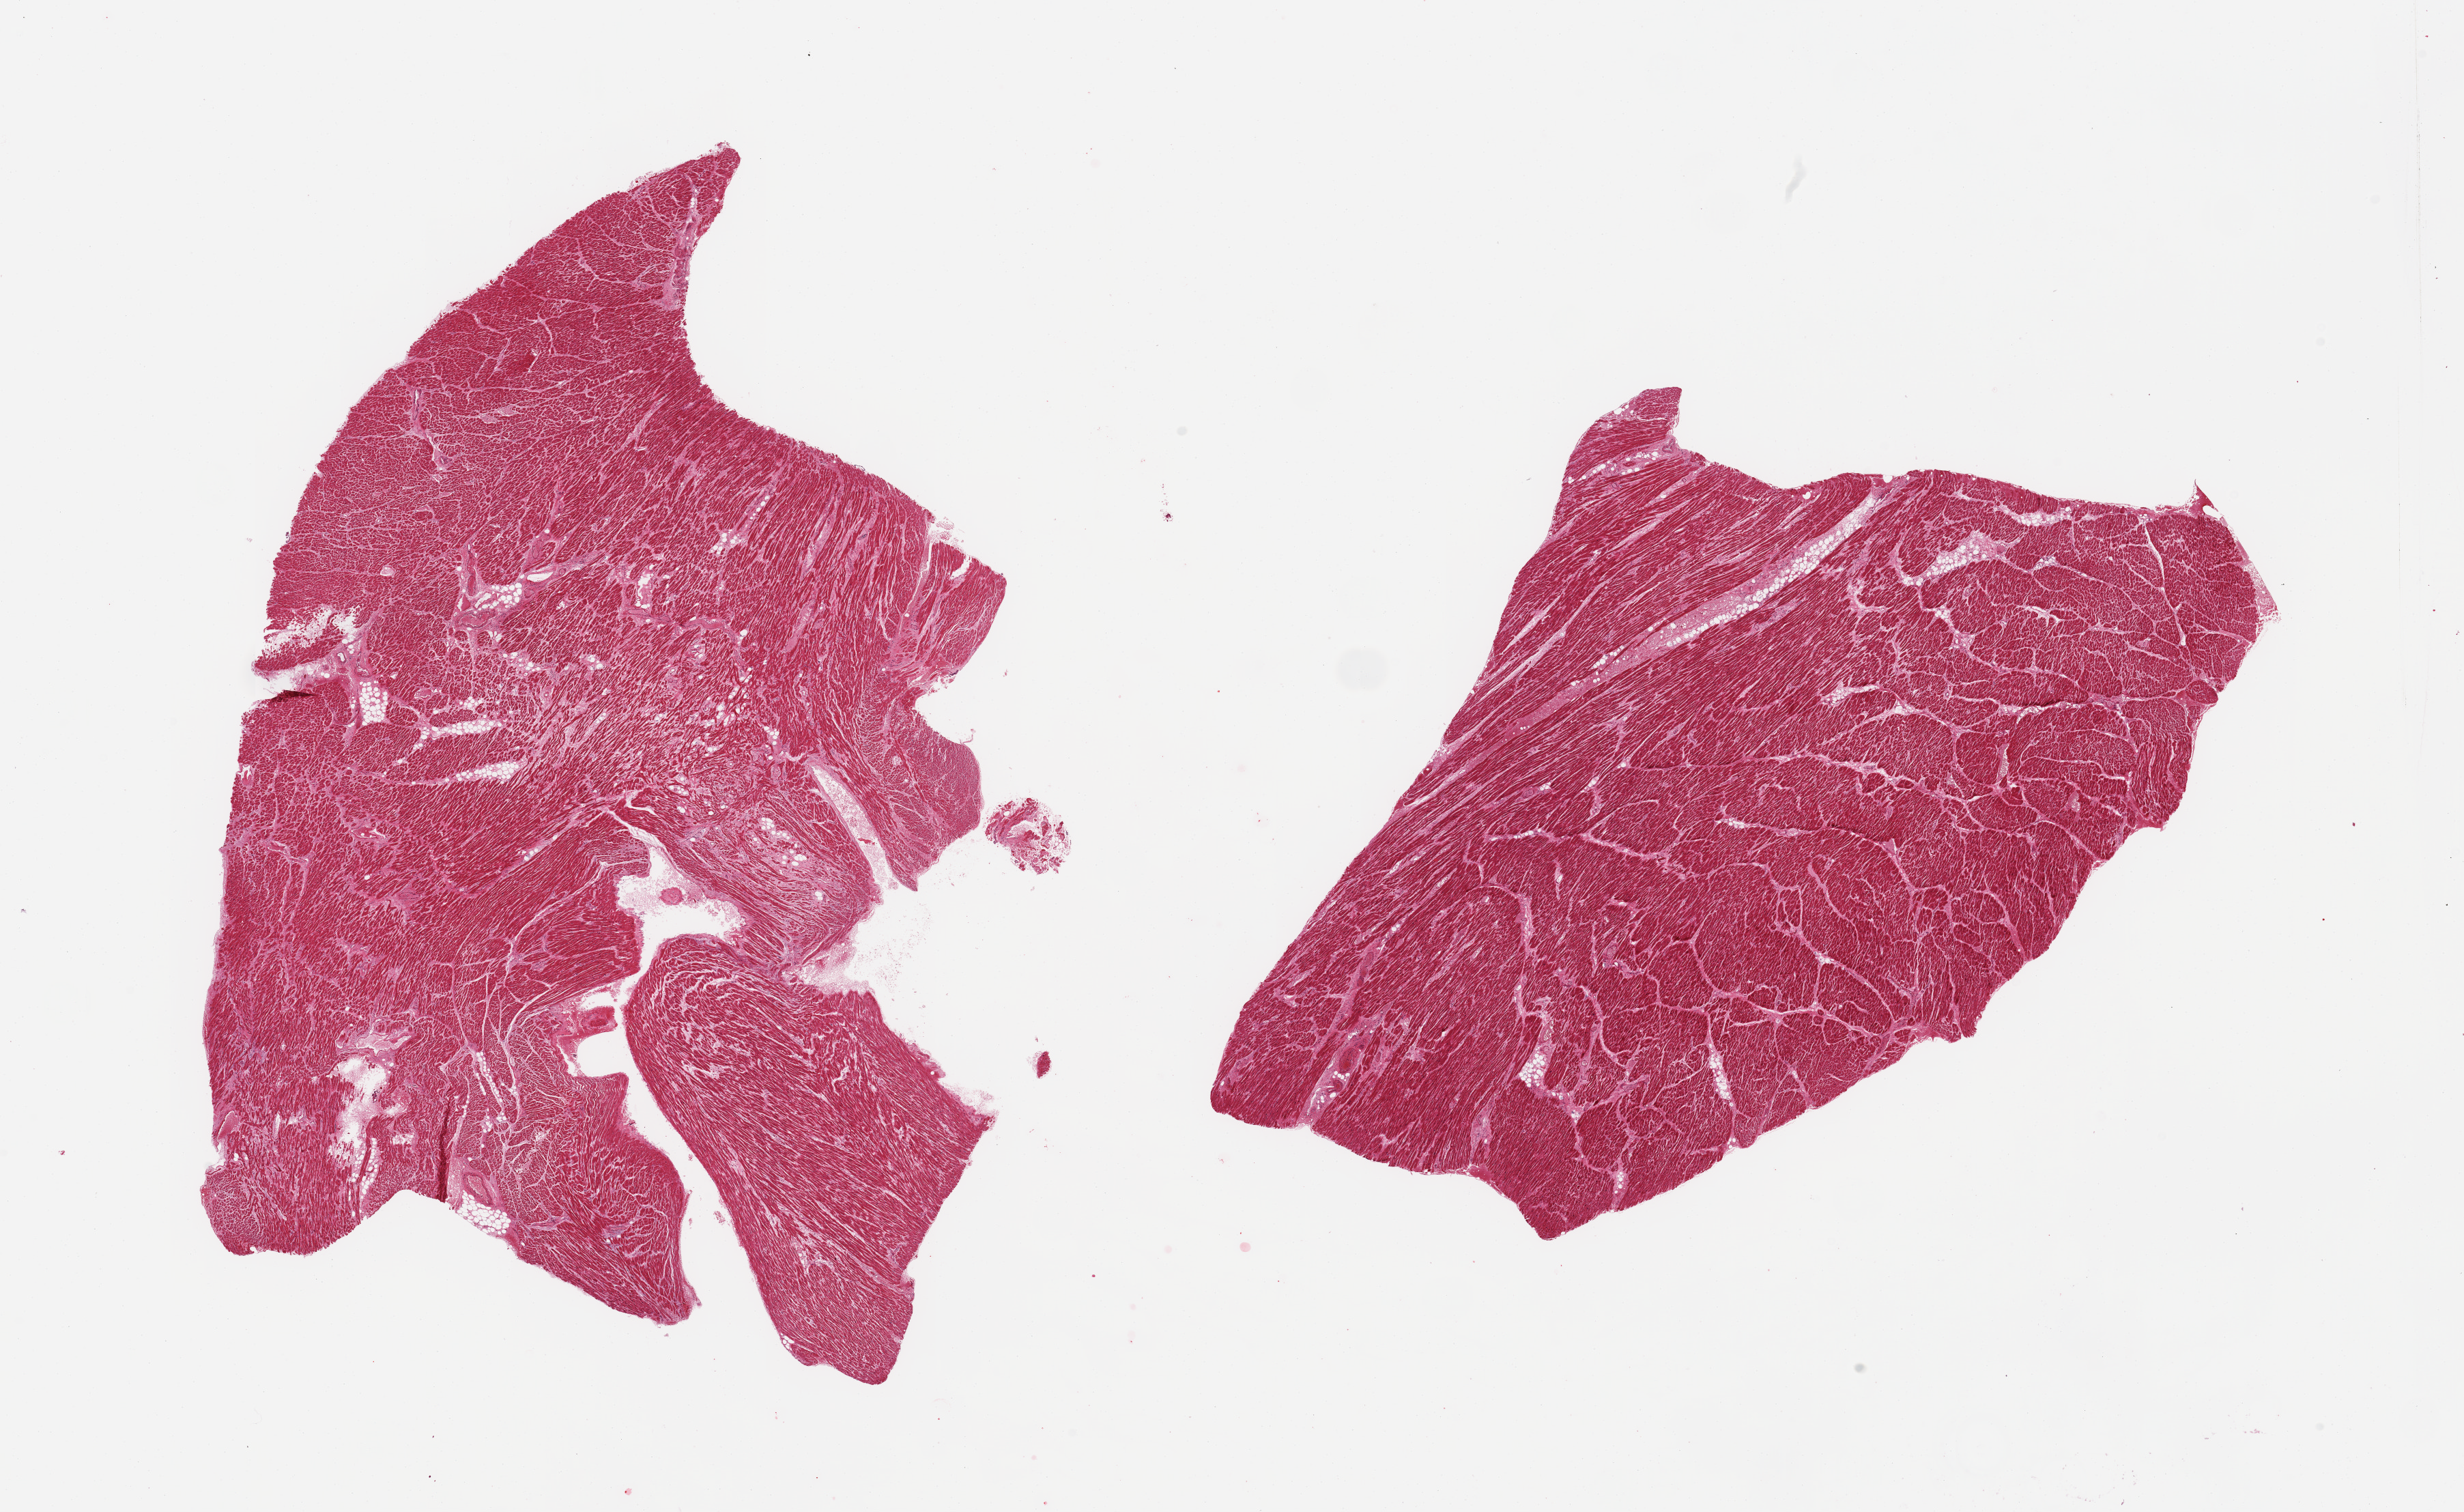
Whole-slide image, H&E stain, brightfield — shown as a low-resolution overview of the whole scanned area (about 28.5 x 17.5 mm); PAXgene-fixed paraffin-embedded (PFPE) section; section of heart (target tissue); tissue donor sample.
* review note (as recorded): 2 pieces; some interstitial fibrosis and minimal intervening fat